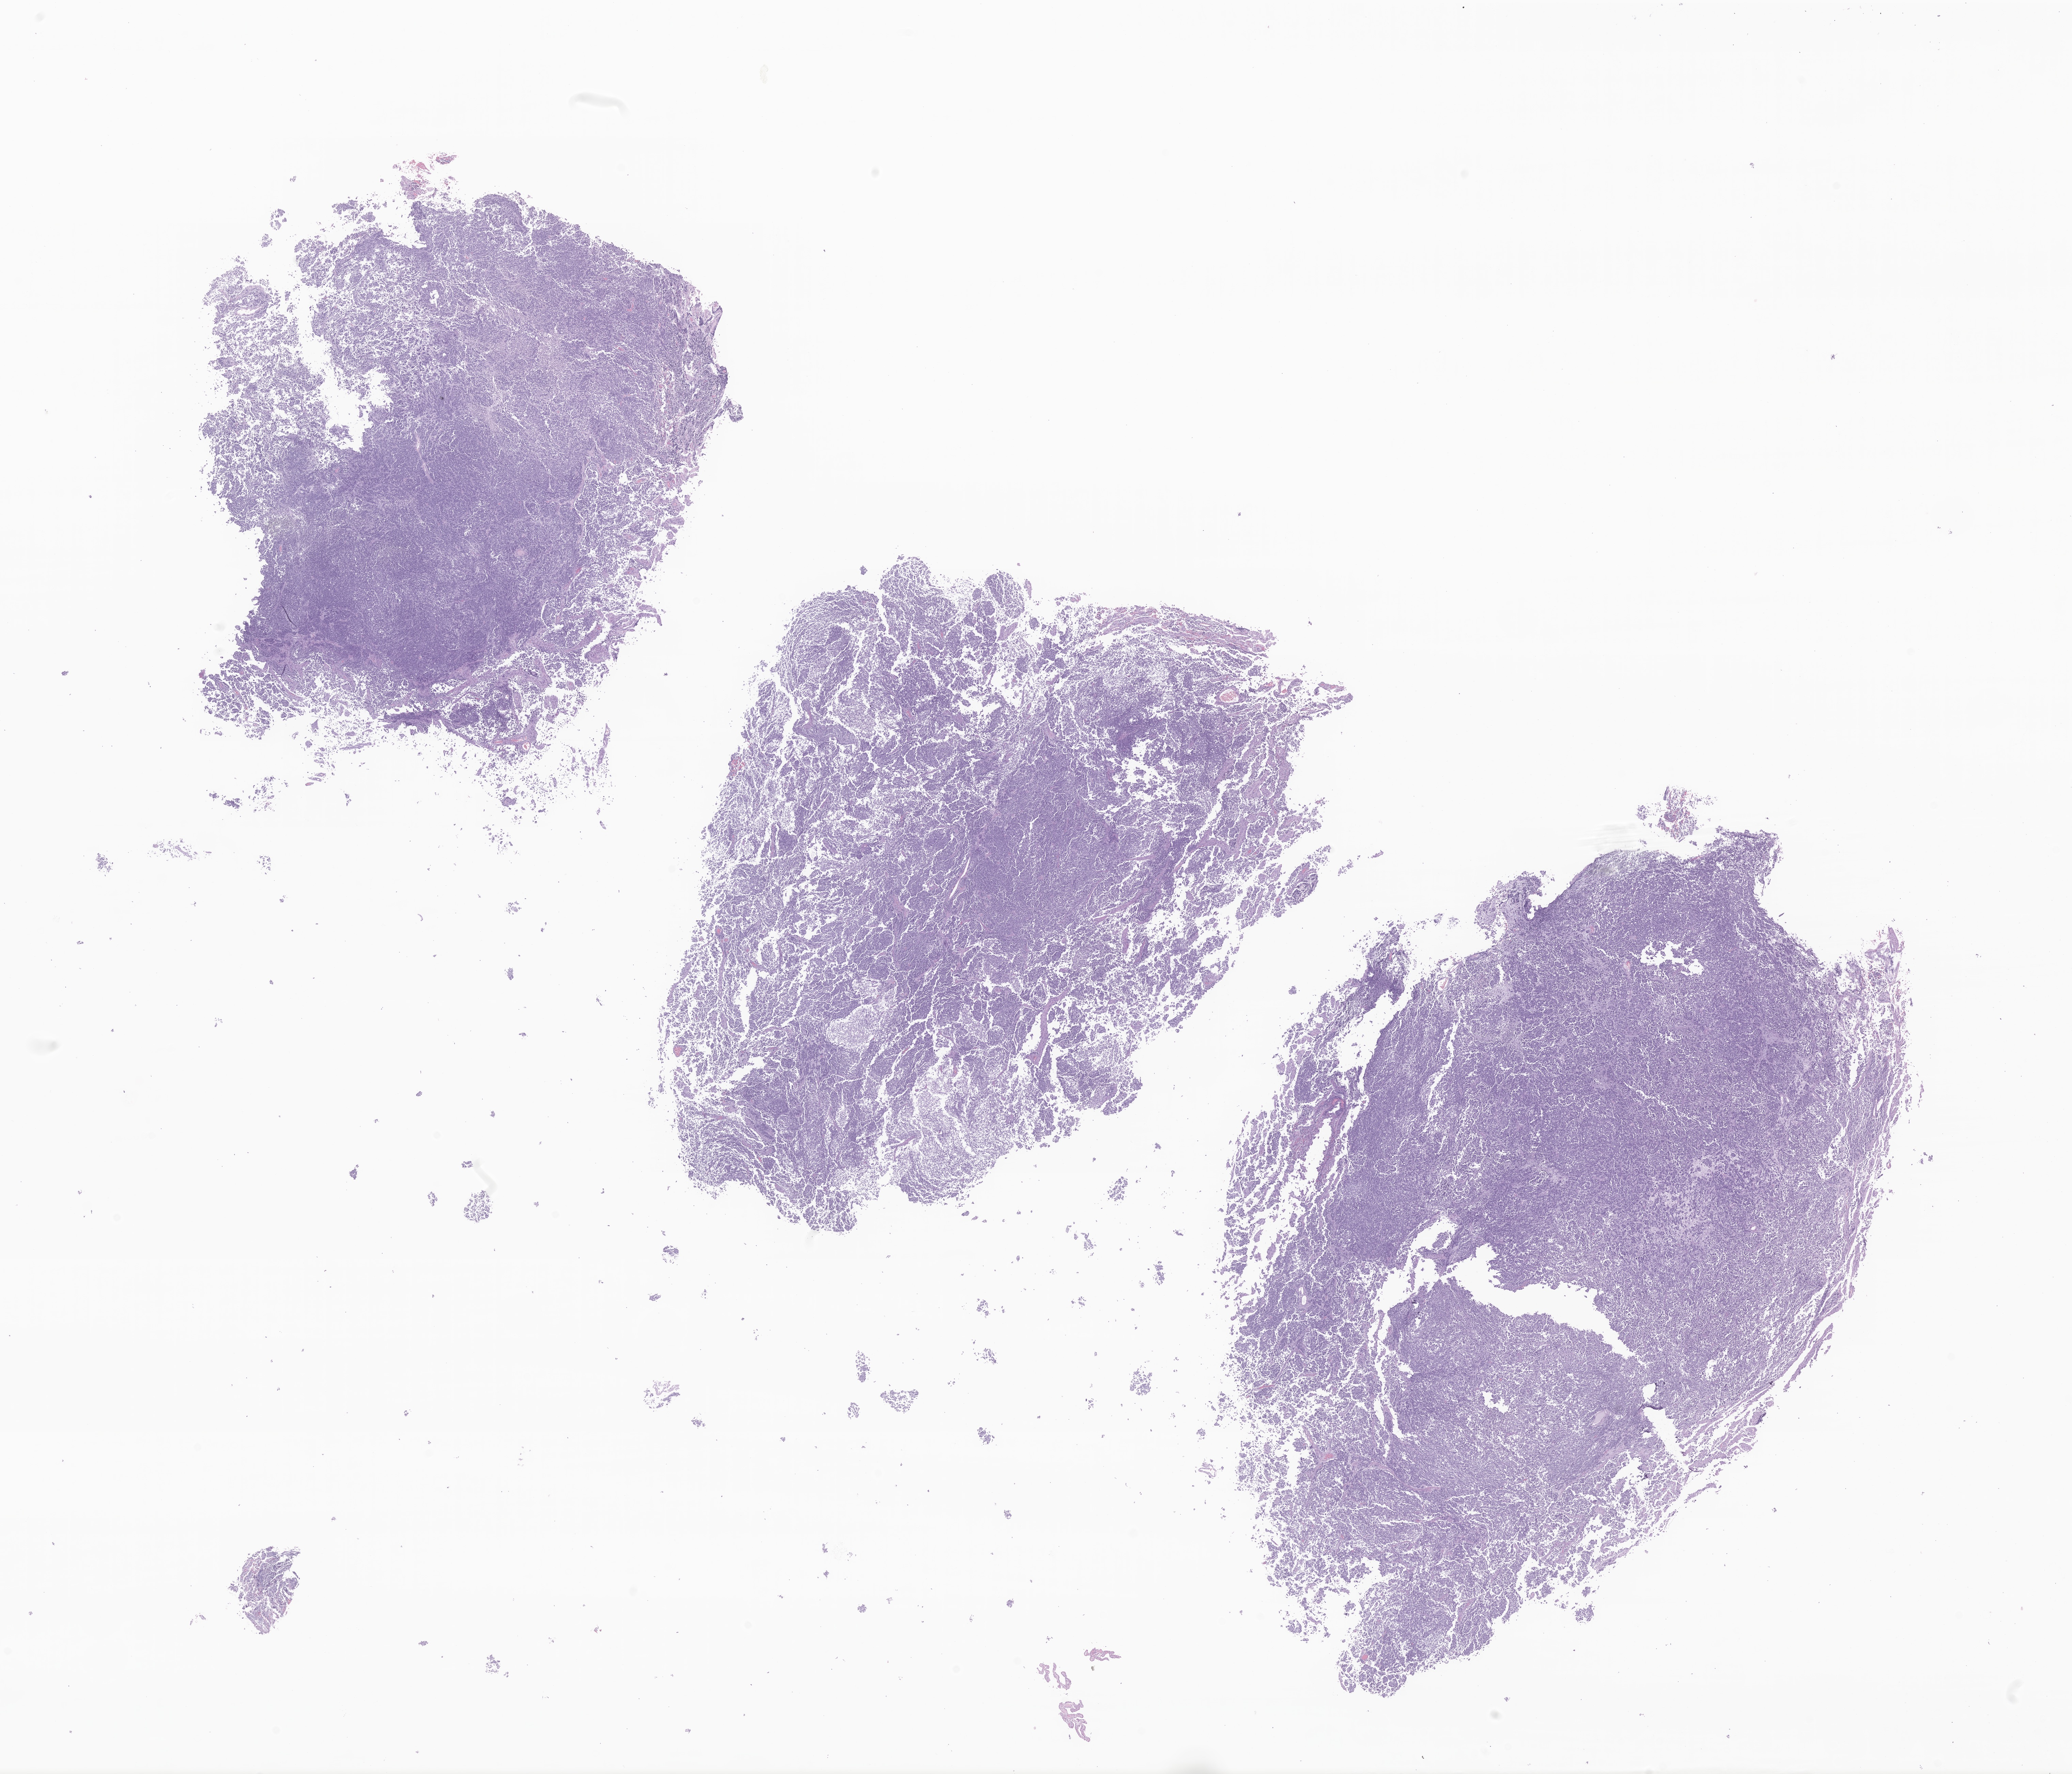
Whole-slide image, haematoxylin and eosin stain of tumor tissue from the brain — low-resolution overview of the scanned area, about 25.6 x 22.0 mm, formalin-fixed, paraffin-embedded (FFPE) tissue. Male patient, age 78 months (6 years 6 months).
• diagnosis (ICD-O-3 morphology term): Glioma, malignant